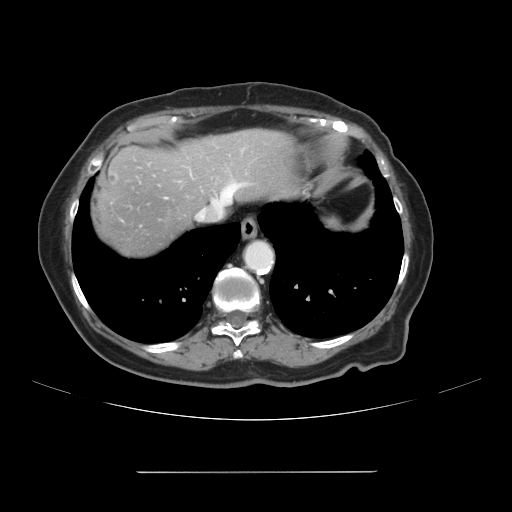
Contrast-enhanced abdominal CT, one axial slice; intravenous contrast given; soft-tissue window (W 400 / L 40 HU); 512 × 512 image matrix. Female patient, age 74 years. Case-level facts recorded for this patient, not image findings: diagnosis: colorectal cancer liver metastases, imaged before liver resection; multiple liver metastases: yes; largest metastasis: 1.1 cm.
Structures marked on this image (manually delineated by an expert):
- hepatic veins: bounding box [x1, y1, x2, y2] px = [212, 185, 238, 209]
- liver: [93, 130, 297, 261]
- planned liver remnant (the part of the liver to remain after resection): [185, 130, 295, 209]
- liver metastasis: [107, 173, 116, 185]
- liver metastasis: [167, 216, 176, 224]